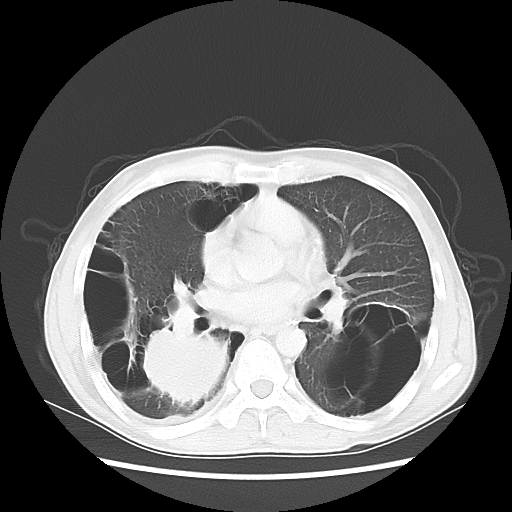
Chest CT, one axial slice. Slice 28 of 57 in the series (ordered by position). Reconstruction kernel LUNG. 140 kVp. Lung window (W 1500 / L -600 HU). 5 mm slice thickness. 512 × 512 image matrix, field of view 351 × 351 mm. Male patient, age 41 years. From the clinical record (not read from this slice): clinical TNM (as recorded): T4 N0 M1a.
Annotated regions visible in this slice (bounding box drawn by a radiologist):
- lung tumour (recorded histology: large cell carcinoma): bounding box [x1, y1, x2, y2] px = [137, 324, 242, 410]